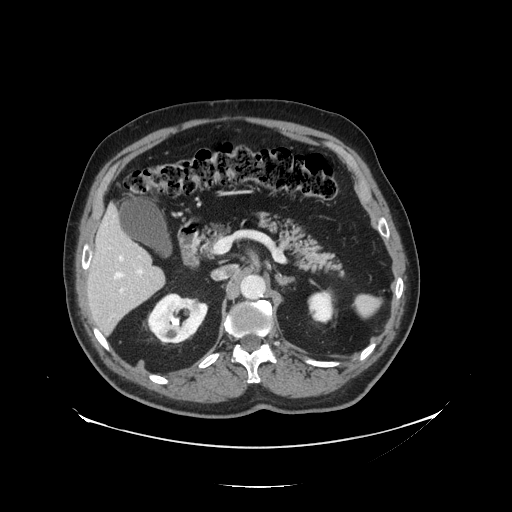
Contrast-enhanced abdominal CT, one axial slice. Position 72 of 138 along the scan axis. Reconstruction kernel STANDARD. Intravenous contrast given. Soft-tissue window (W 400 / L 40 HU). 2.5 mm slice thickness. 512 × 512 image matrix, field of view 497 × 497 mm. Male patient, age 77 years. From the clinical record (not read from this slice): diagnosis: colorectal cancer liver metastases, imaged before liver resection; multiple liver metastases: no; largest metastasis: 1.5 cm; disease in both lobes: no.
Outlined on this slice (manually delineated by an expert):
- hepatic veins: bounding box <114,256,124,278> (left, top, right, bottom; pixels)
- liver: <87,210,165,335>
- planned liver remnant (the part of the liver to remain after resection): <87,210,154,287>
- portal vein (with intrahepatic branches): <119,268,143,293>